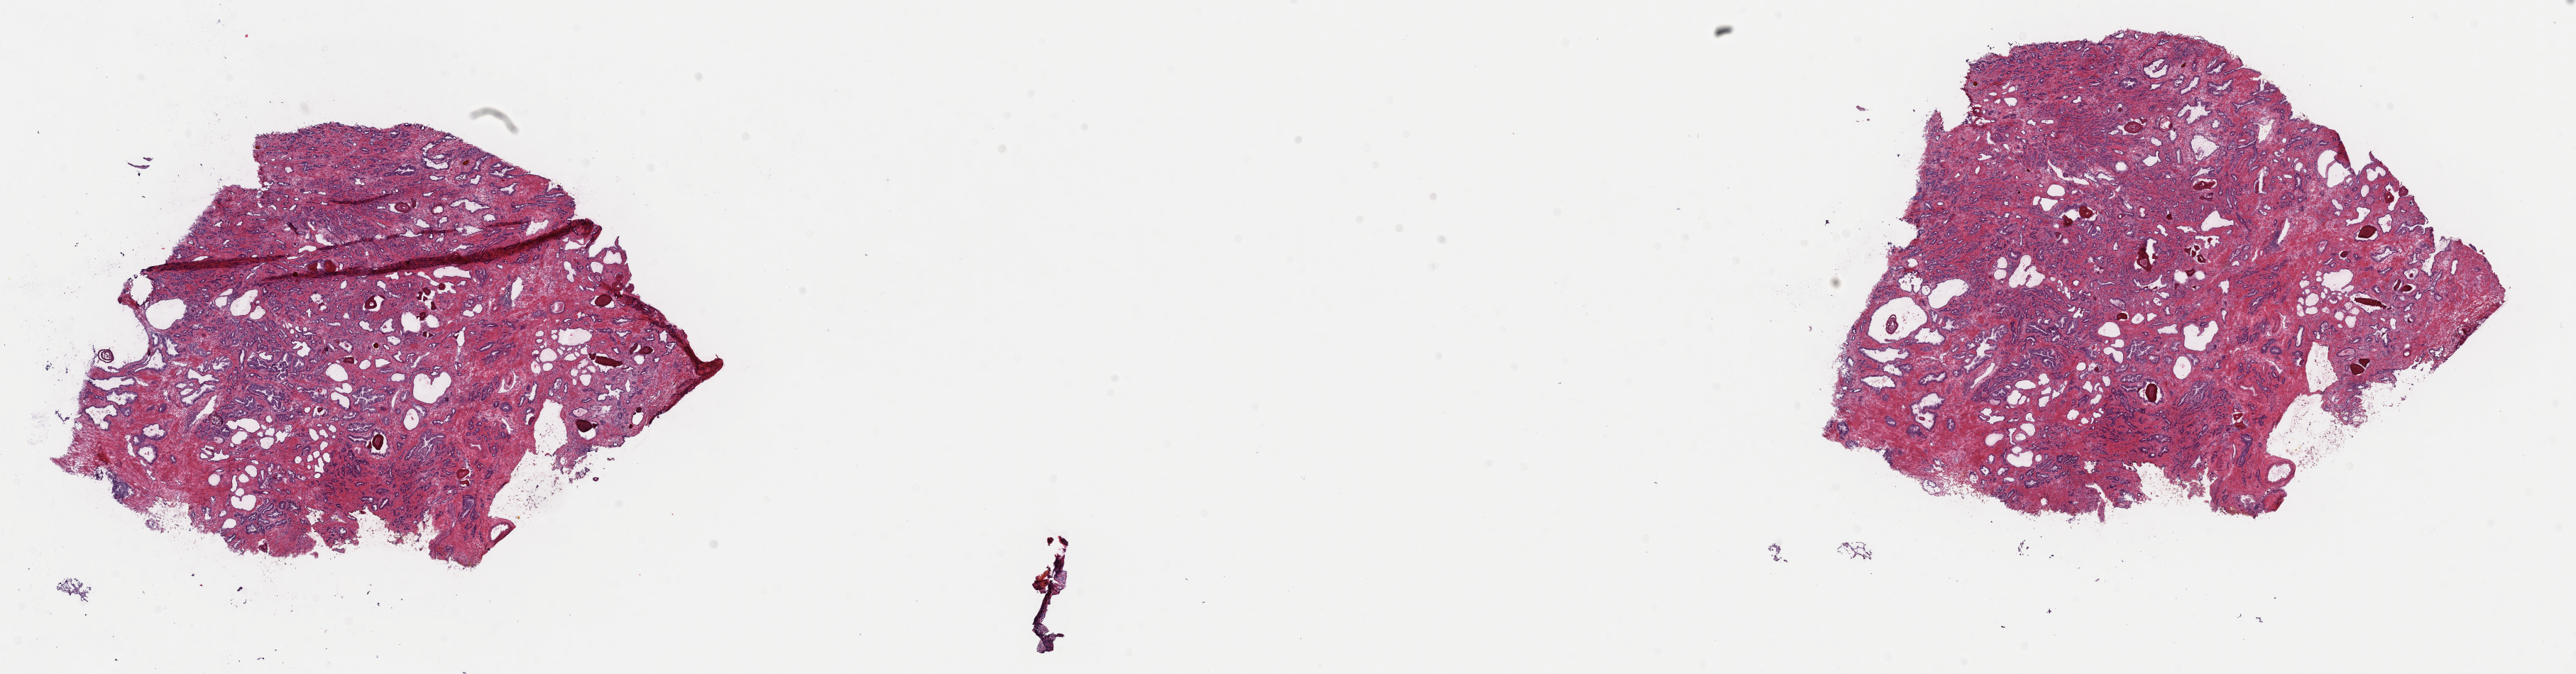
Whole-slide histology image, H&E-stained — a low-resolution overview of the entire scanned area, about 28.7 x 7.5 mm (slide scanned at 40x). Frozen section from the top of the tissue portion. Primary tumour sample from the prostate. Male patient; age at initial diagnosis 50 years. Gleason score: 7 (3+4). Composition of this section per pathologist review: tumour cells 70%, tumour nuclei 70%, normal cells 0%, stromal cells 30%, necrosis 0%. Infiltration values recorded for this section: lymphocyte infiltration 40%, monocyte infiltration 20%, neutrophil infiltration 20%.
- laterality: bilateral
- lymph nodes positive (case pathology): 0 of 12 examined
- diagnosis: Adenocarcinoma, NOS (prostate gland)